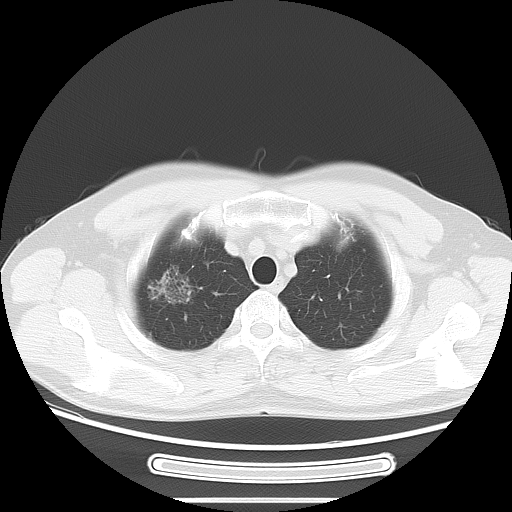
Chest CT, one axial slice; position 57 of 68 along the scan axis; 120 kVp; lung window (W 1500 / L -600 HU); 512 × 512 image matrix, field of view 382 × 382 mm. Male patient, age 53 years. Case-level facts recorded for this patient, not image findings: clinical TNM (as recorded): T1c N0 M0; histopathological grade: G2.
Annotated regions visible in this slice (bounding box drawn by a radiologist):
- lung tumour (recorded histology: adenocarcinoma): bounding box [x1, y1, x2, y2] px = [144, 262, 200, 310]